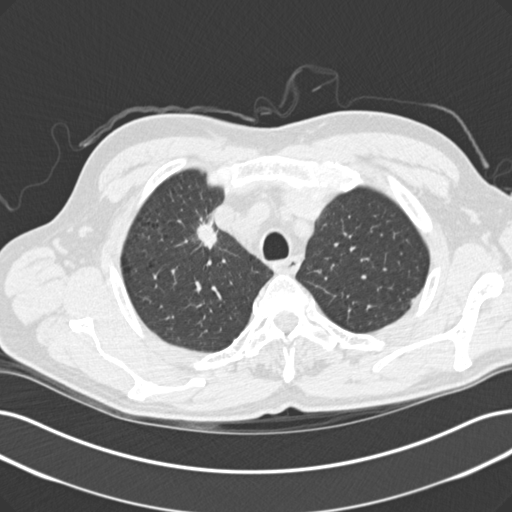
Low-dose screening chest CT, one axial slice; slice 121 of 152 in the series (ordered by position); reconstruction kernel B30f; 120 kVp; lung window (W 1500 / L -600 HU); 512 × 512 image matrix, field of view 365 × 365 mm.
Annotated regions visible in this slice (outlined manually by an expert reader):
- lesion 1 (tumor, upper lobe of right lung): box from (x=197, y=219) to (x=217, y=249) px